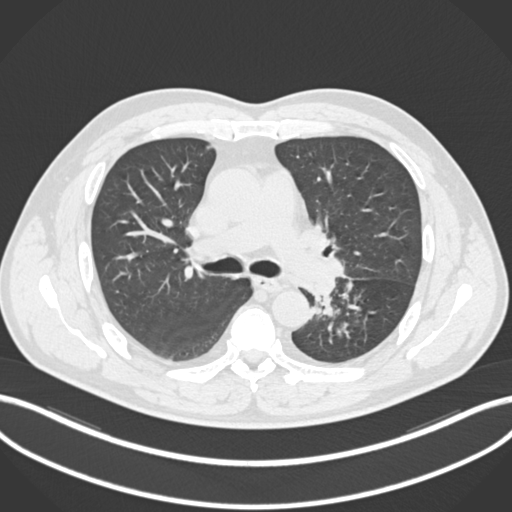
Chest CT, one axial slice. Slice 141 of 223 in the series (ordered by position). Reconstruction kernel B30f. 120 kVp. Lung window (W 1500 / L -600 HU). 1 mm slice thickness. 512 × 512 image matrix. Male patient, age 50 years. Case-level facts recorded for this patient, not image findings: clinical TNM (as recorded): T2a N3 M0.
Annotated regions visible in this slice (bounding box drawn by a radiologist):
- lung tumour (recorded histology: squamous cell carcinoma): bounding box <305,272,338,302> (left, top, right, bottom; pixels)